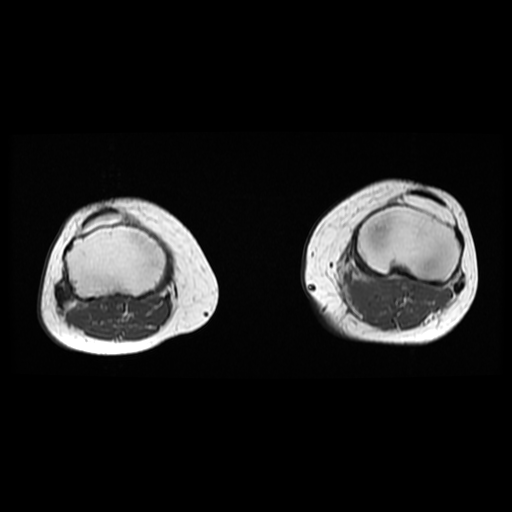
MRI of an extremity soft-tissue mass, one axial slice; position 25 of 38 along the scan axis; 6 mm slice thickness; 512 × 512 image matrix, field of view 330 × 330 mm. Female patient. From the clinical record (not read from this slice): histological type: extraskeletal high grade osteogenic sarcoma; grade: high; site of the primary tumour: left calf.
Outlined on this slice (expert manual segmentation):
- gross tumour volume (mass): bounding box <346,276,389,307> (left, top, right, bottom; pixels)